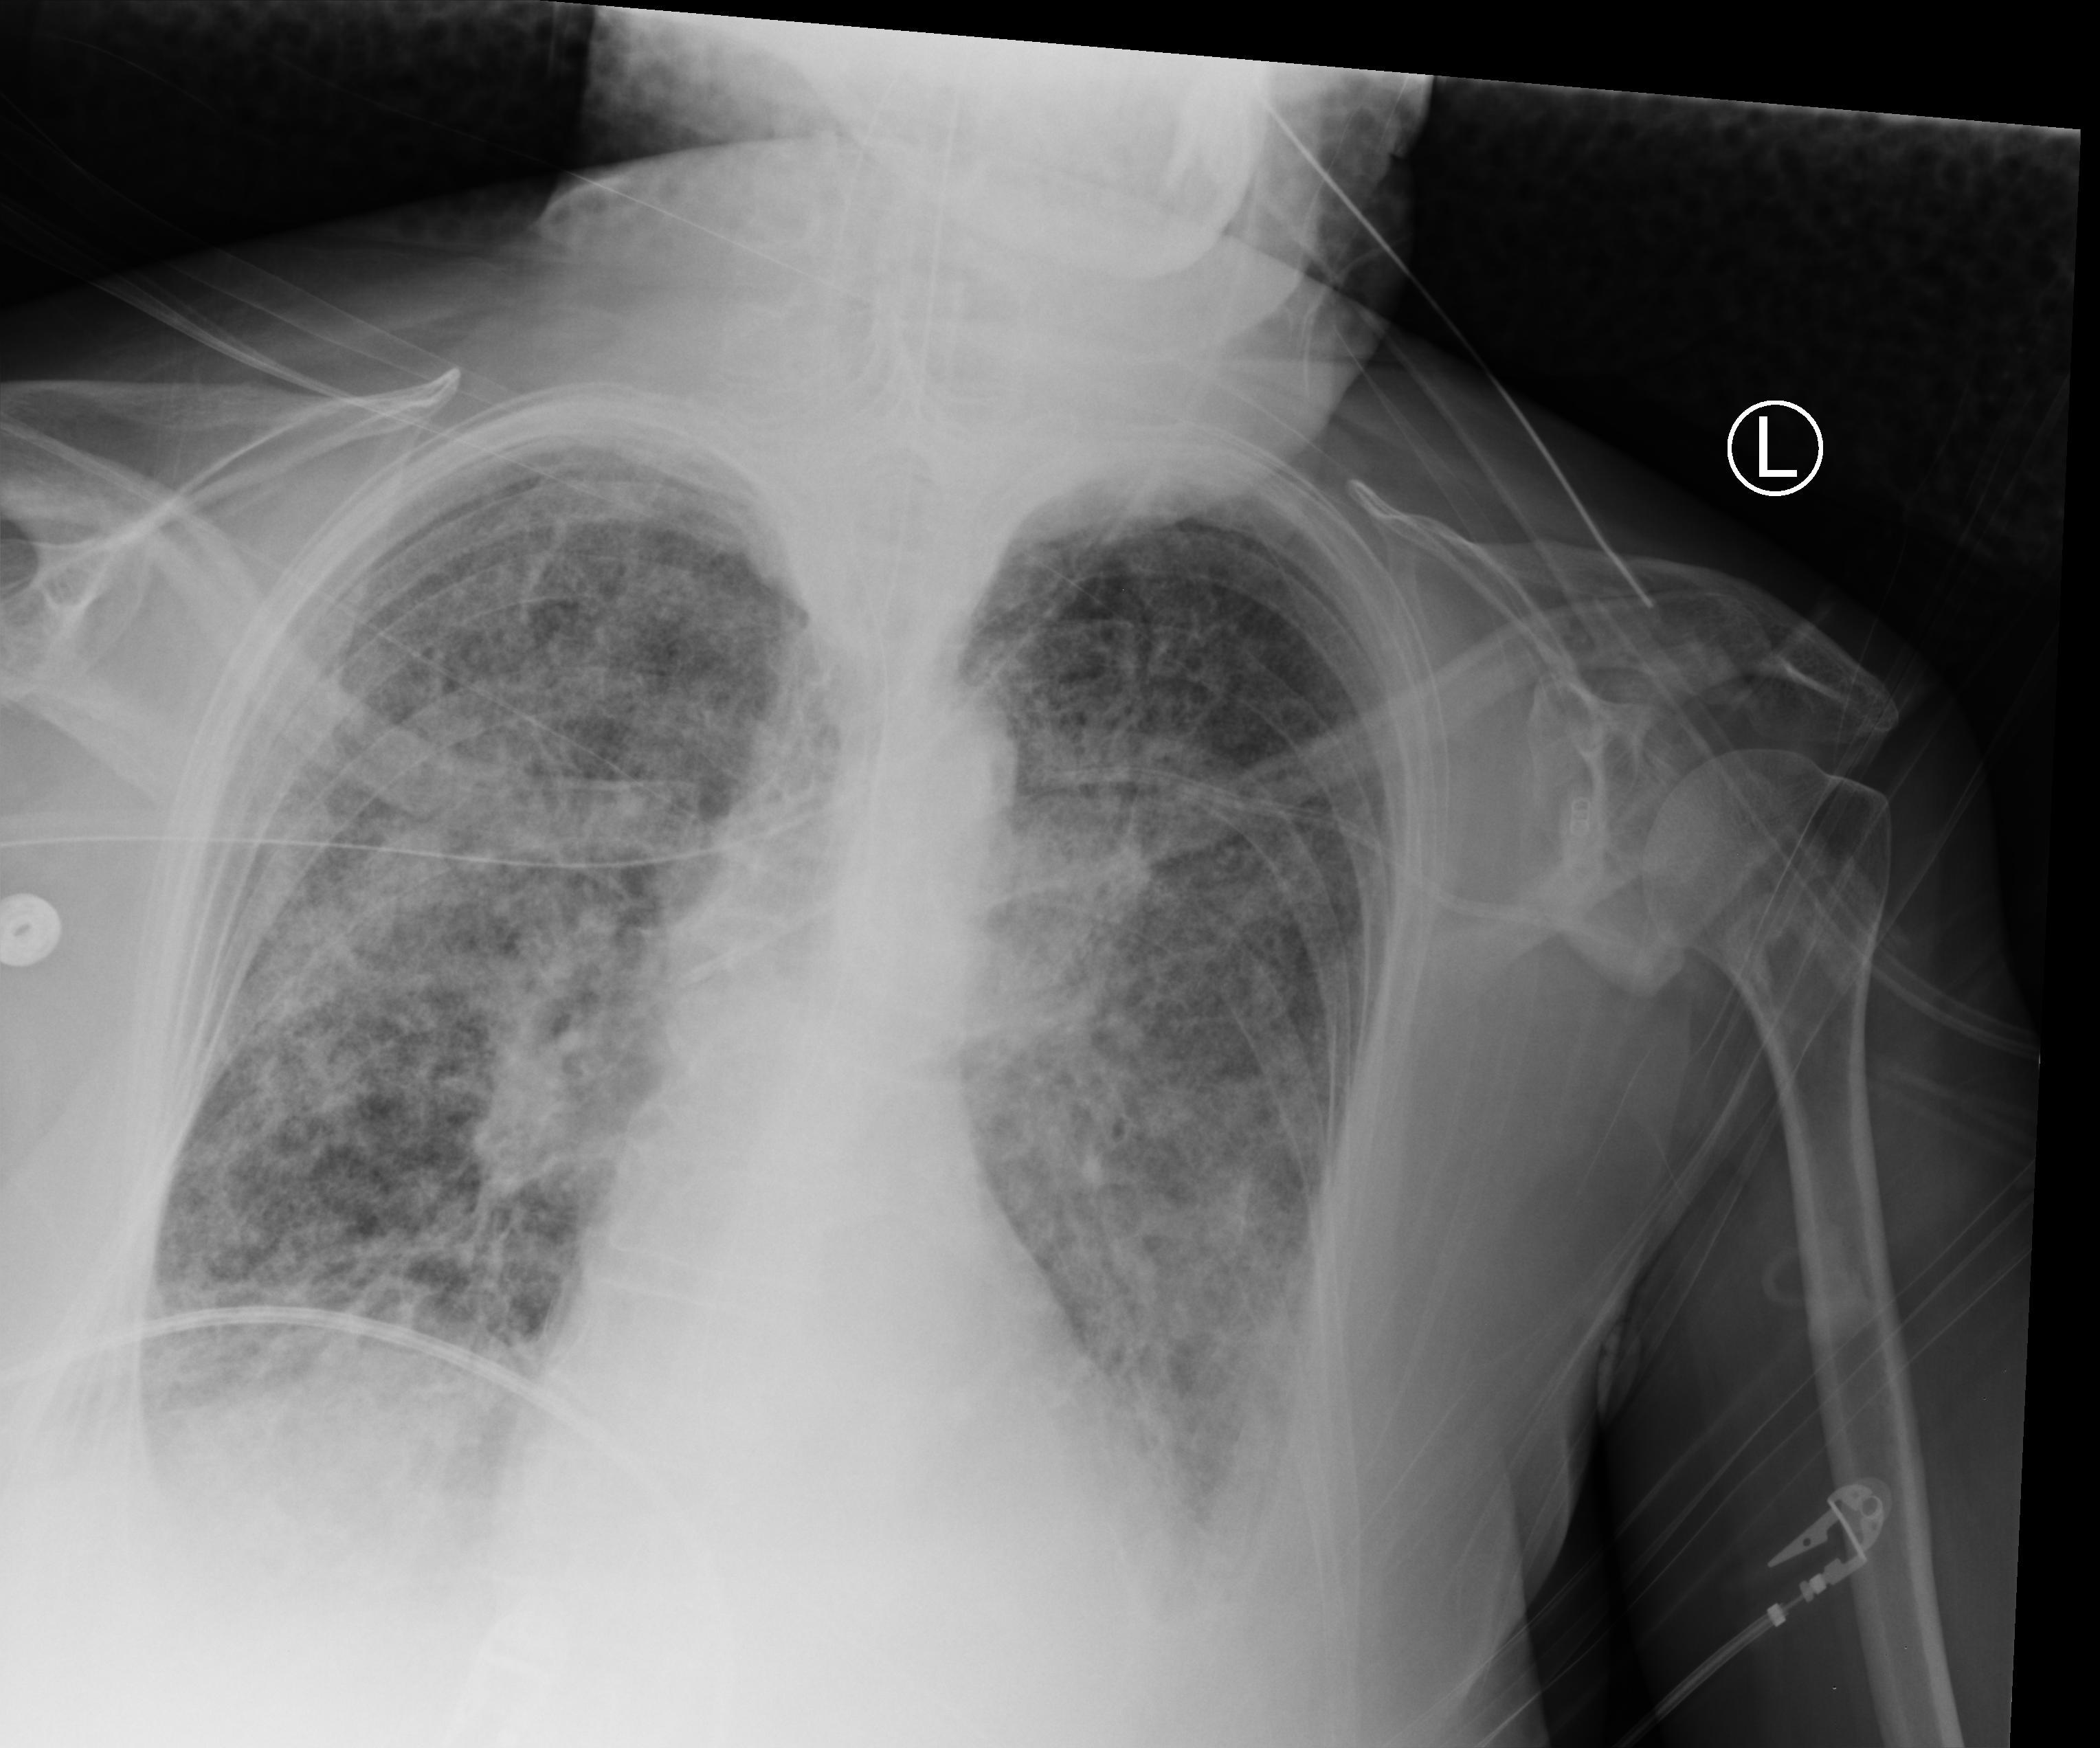
Chest X-ray (portable), anteroposterior (AP) projection. Female patient hospitalised with COVID-19, age 75–90 years.
Hospital-stay facts (about this admission, not read from this image; timing relative to this image not recorded): admitted to intensive care during this hospital stay: yes; hypertension (admission record): yes; mechanically ventilated during this hospital stay: yes.